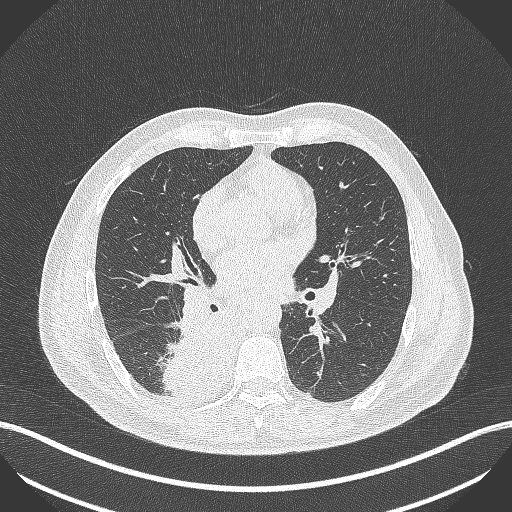
Chest CT, one axial slice; position 240 of 451 along the scan axis; reconstruction kernel B70f; lung window (W 1500 / L -600 HU); 512 × 512 image matrix, field of view 400 × 400 mm. Male patient, age 61 years. Case-level facts recorded for this patient, not image findings: clinical TNM (as recorded): T1 N0 M0; histopathological grade: G3.
Structures marked on this image (rectangle marked by the reading radiologist):
- lung tumour (recorded histology: small cell carcinoma): bounding box <158,310,232,401> (left, top, right, bottom; pixels)